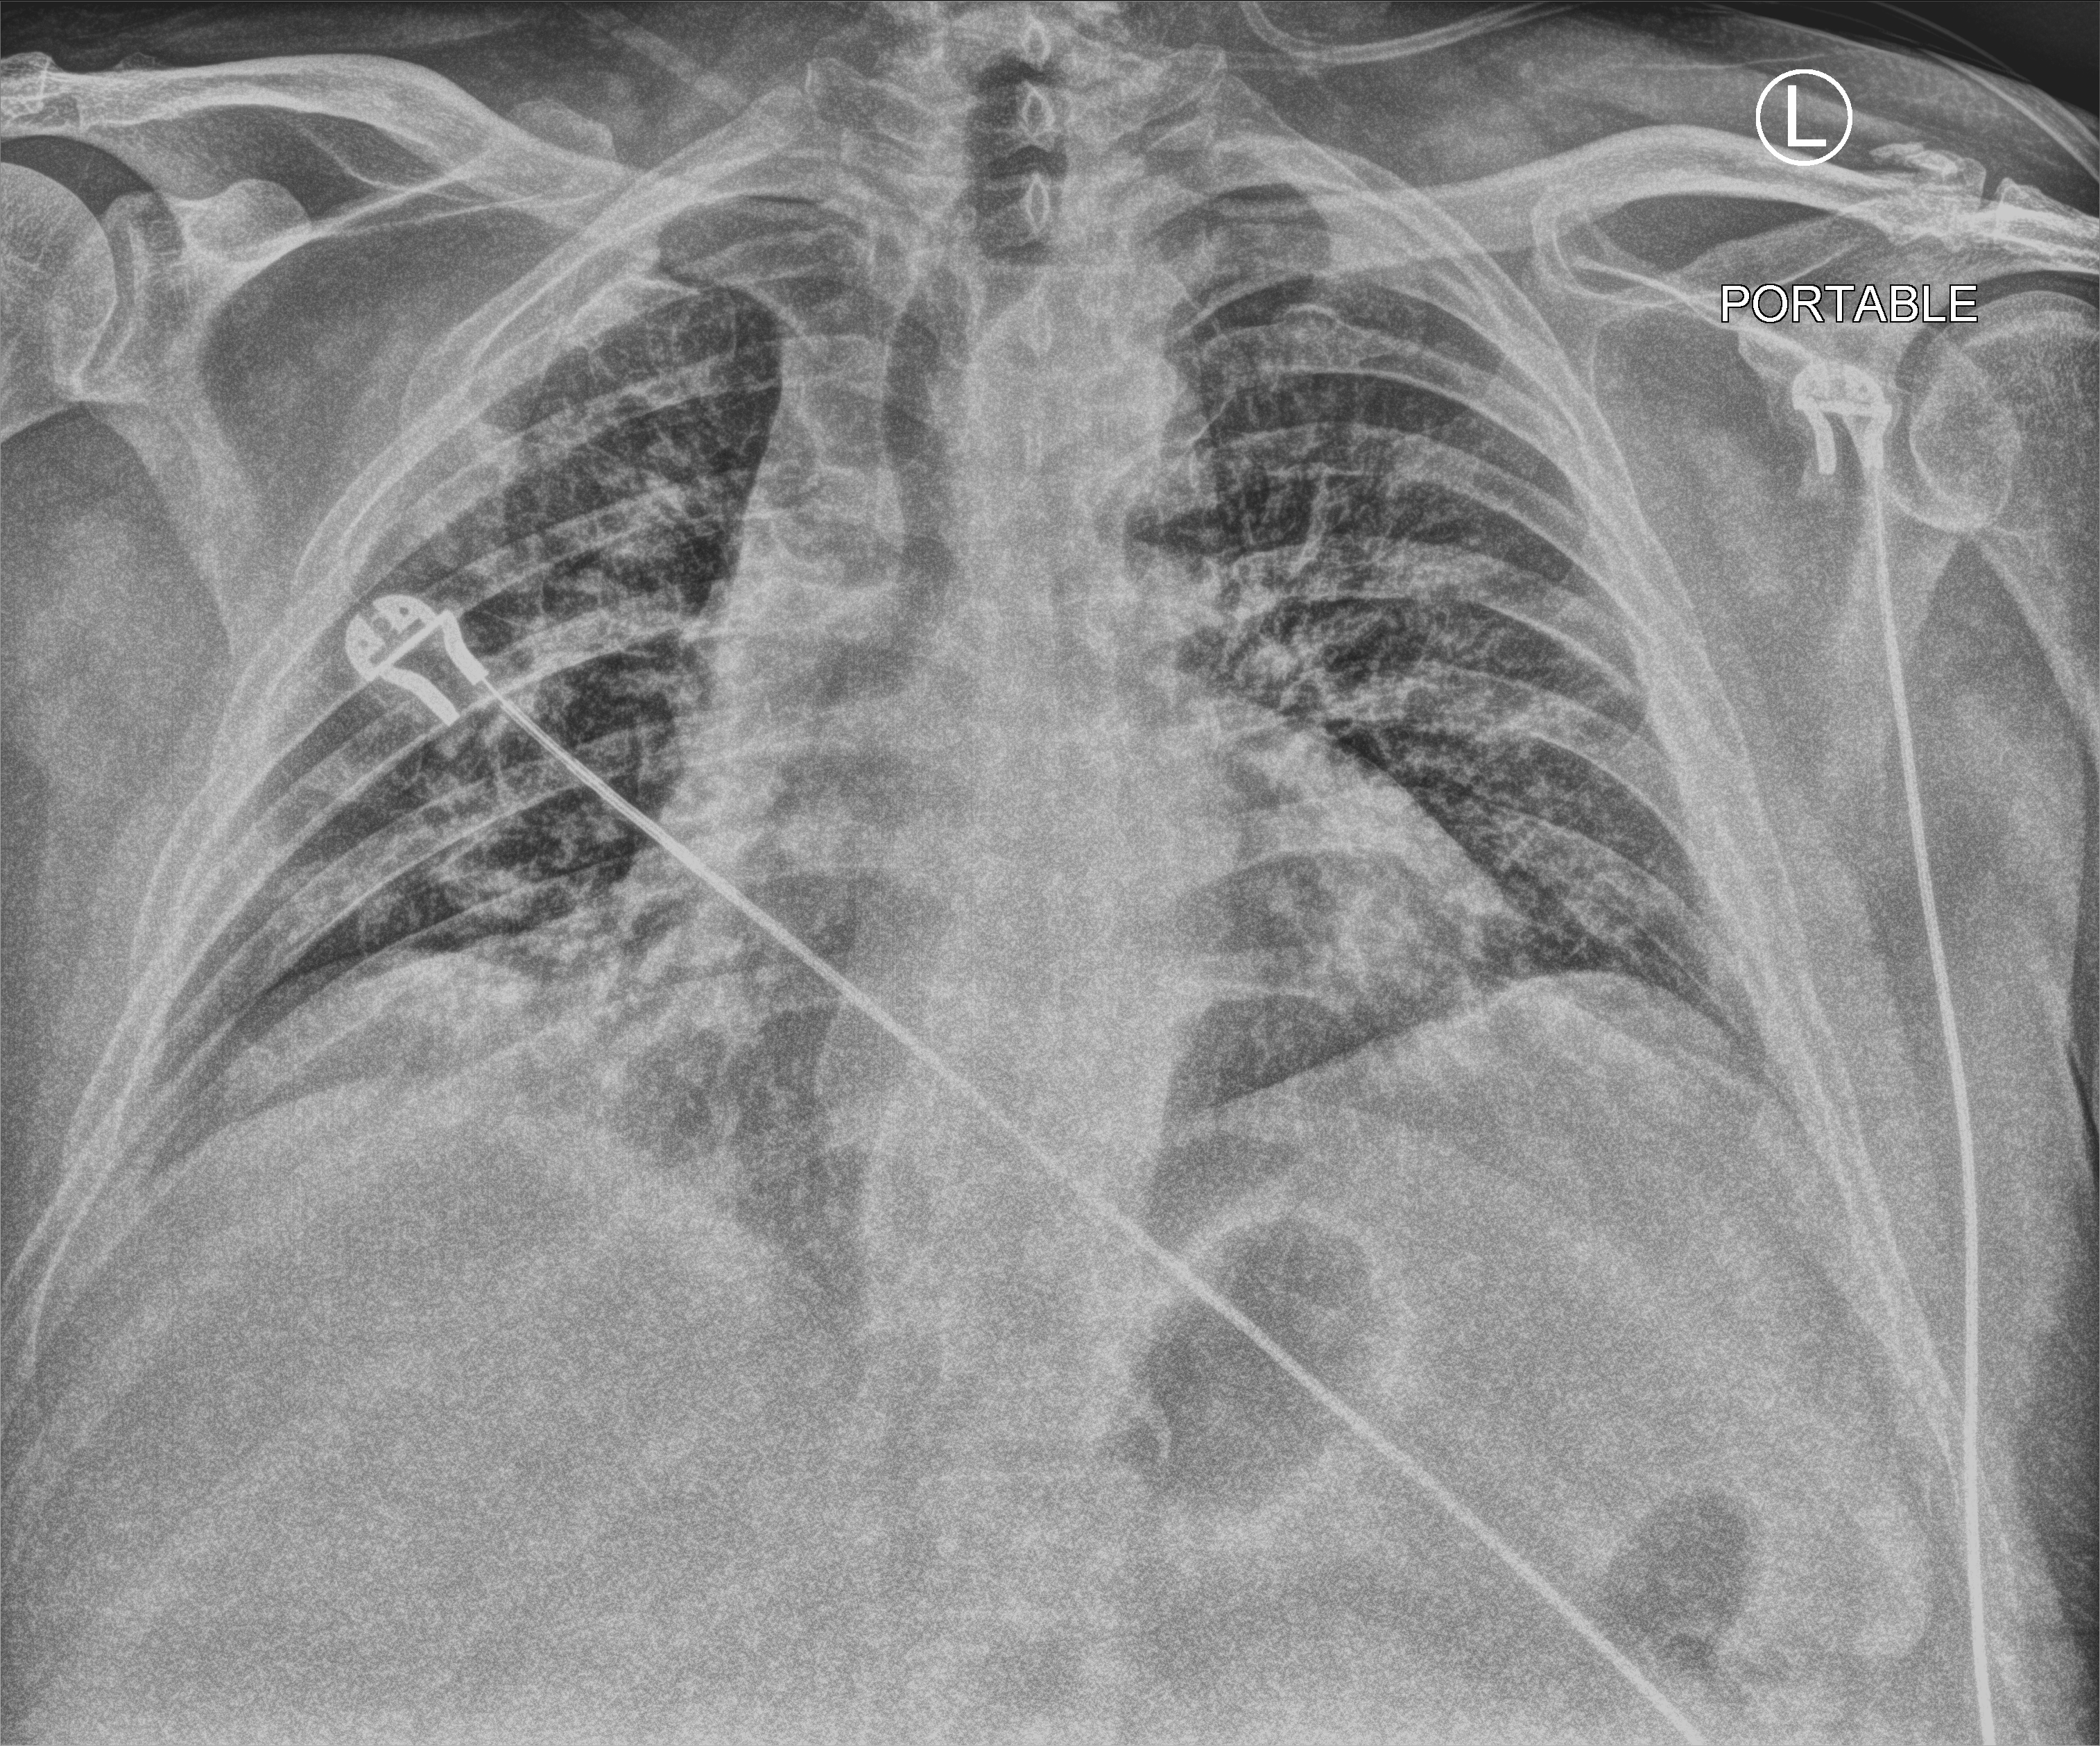
Chest X-ray (portable). Patient hospitalised with COVID-19; male, aged 18–59 years.
From the hospital-stay record, not from the radiograph (when in the stay this image was taken is not recorded): chronic kidney disease (admission record): no.